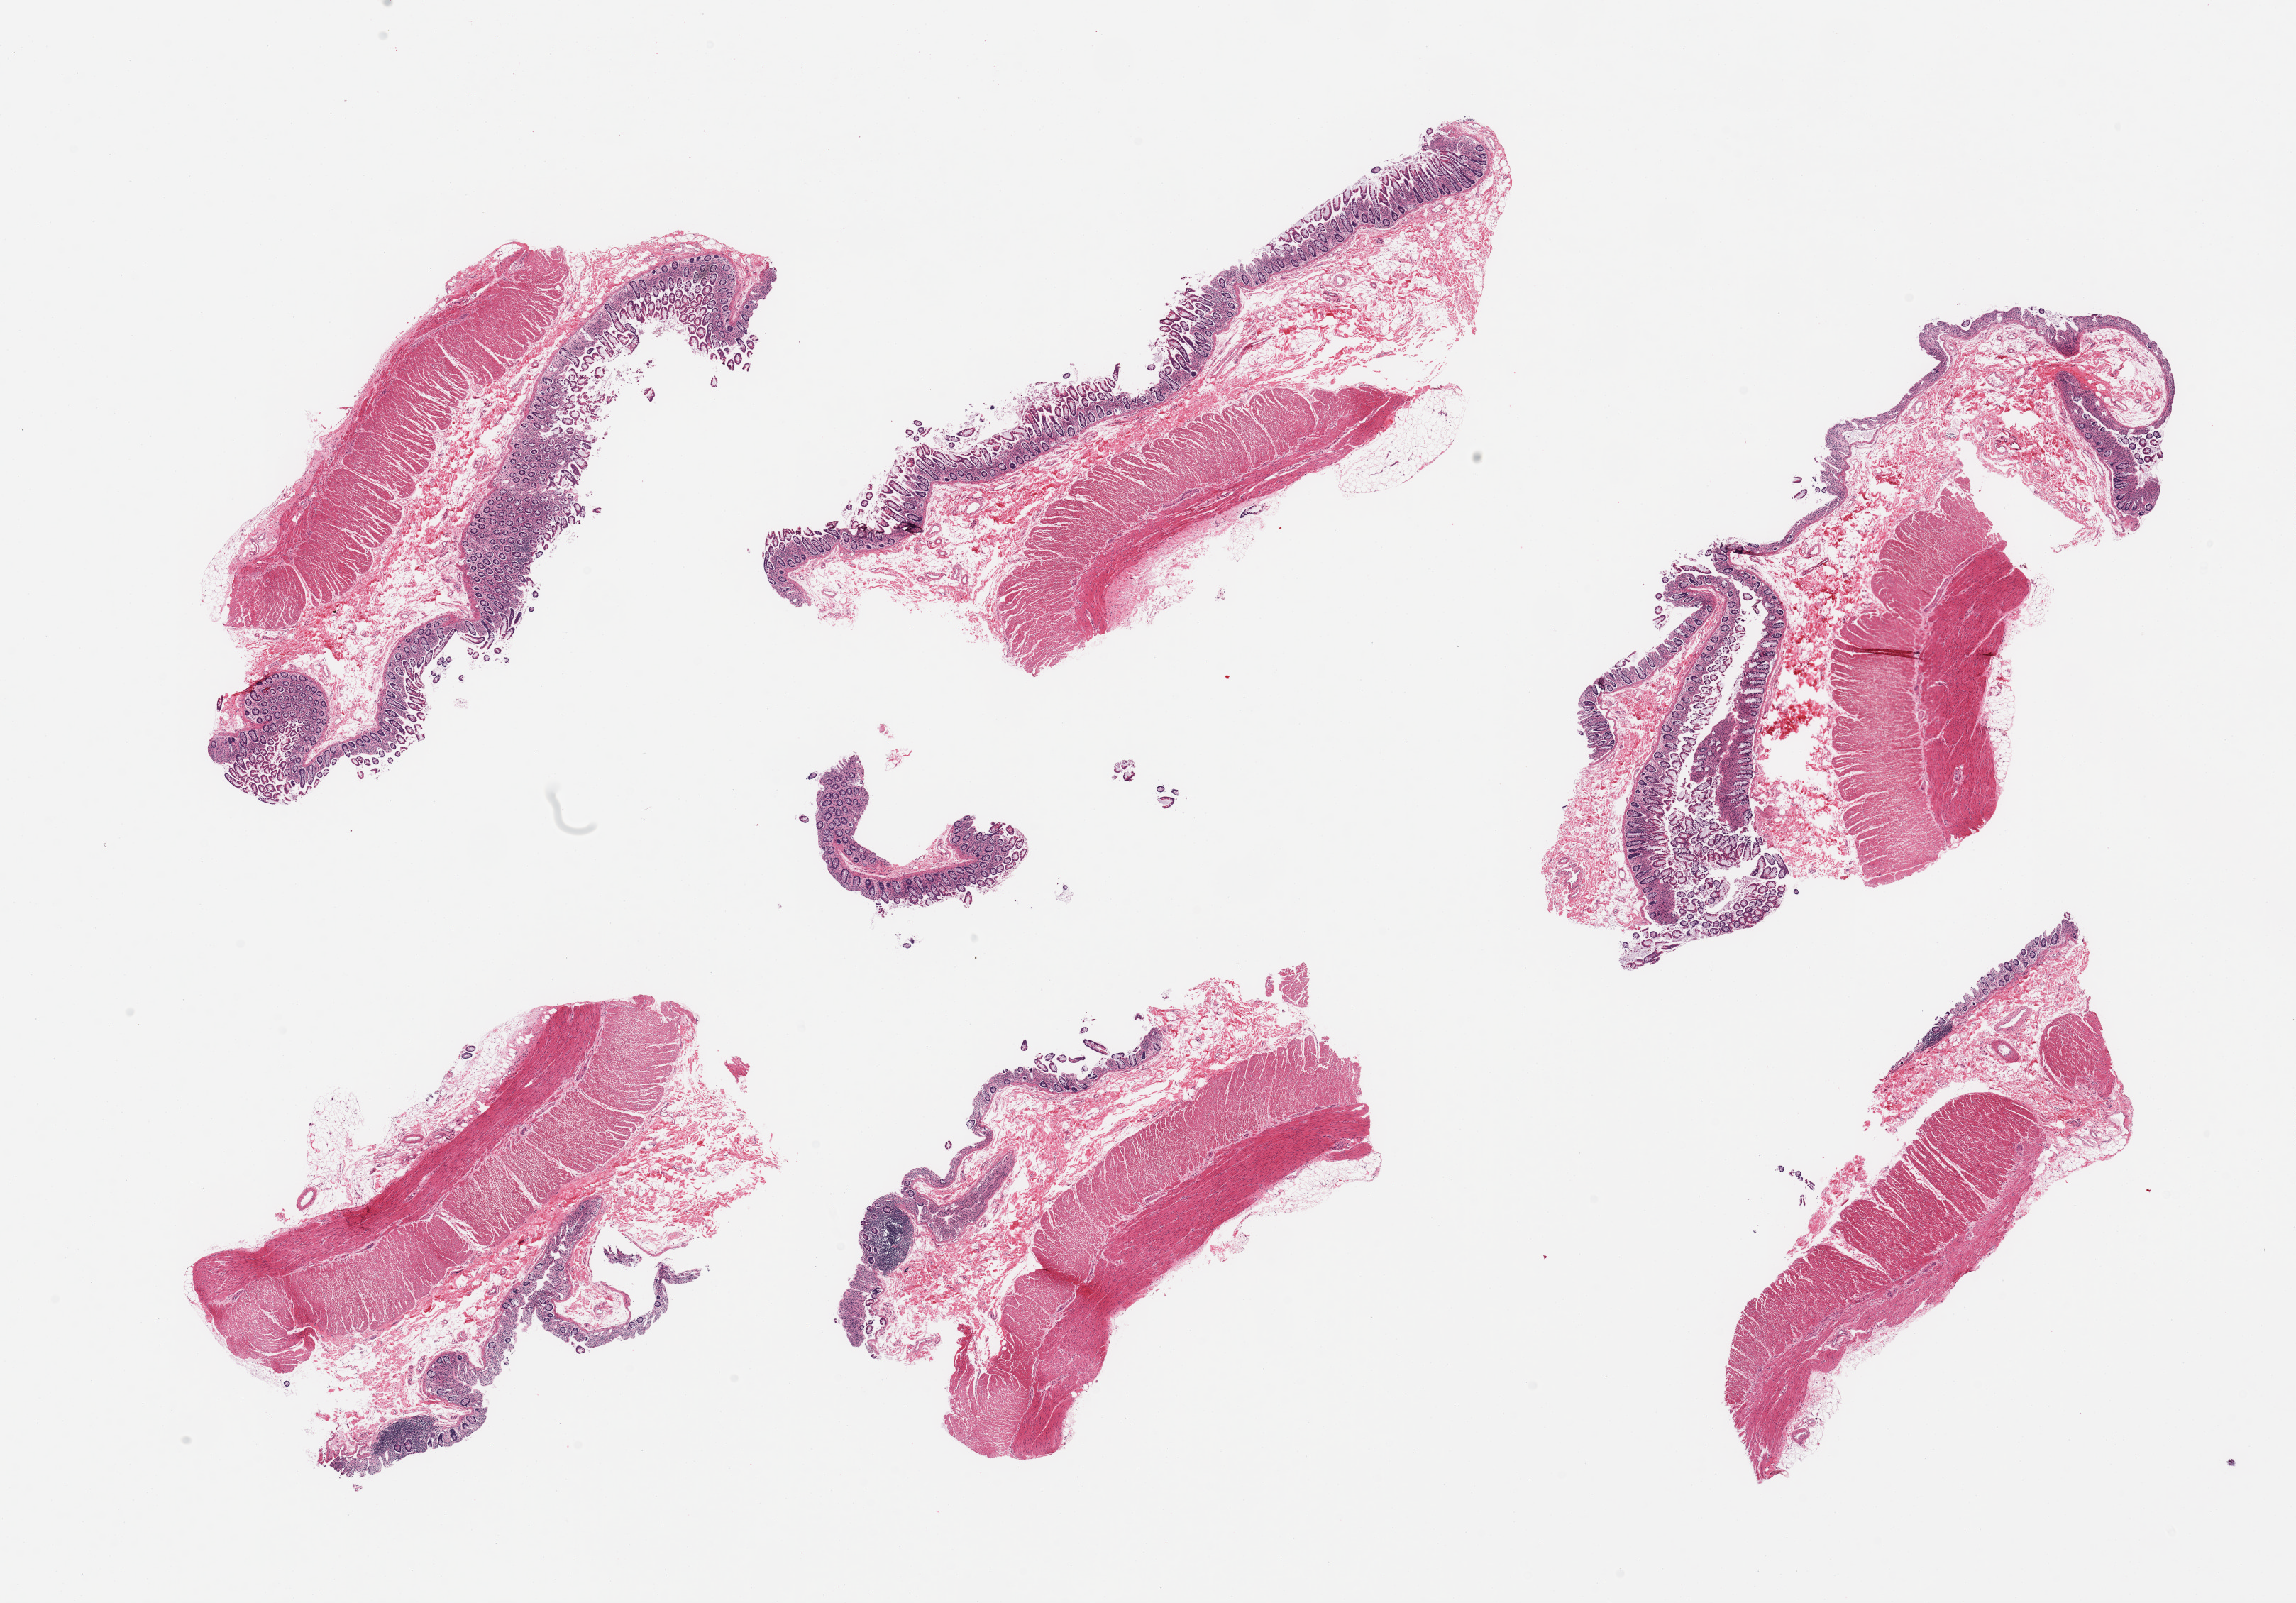
Digitized haematoxylin and eosin-stained section — whole scanned area (about 25.6 x 17.9 mm, slide scanned at 20x) shown as a low-resolution overview, PAXgene-fixed, paraffin-embedded tissue, target tissue: transverse colon, tissue donor sample. Donor: male.
* reviewer comment on this tissue sample: 6 pieces; moderately autolyzed mucosa and muscularis